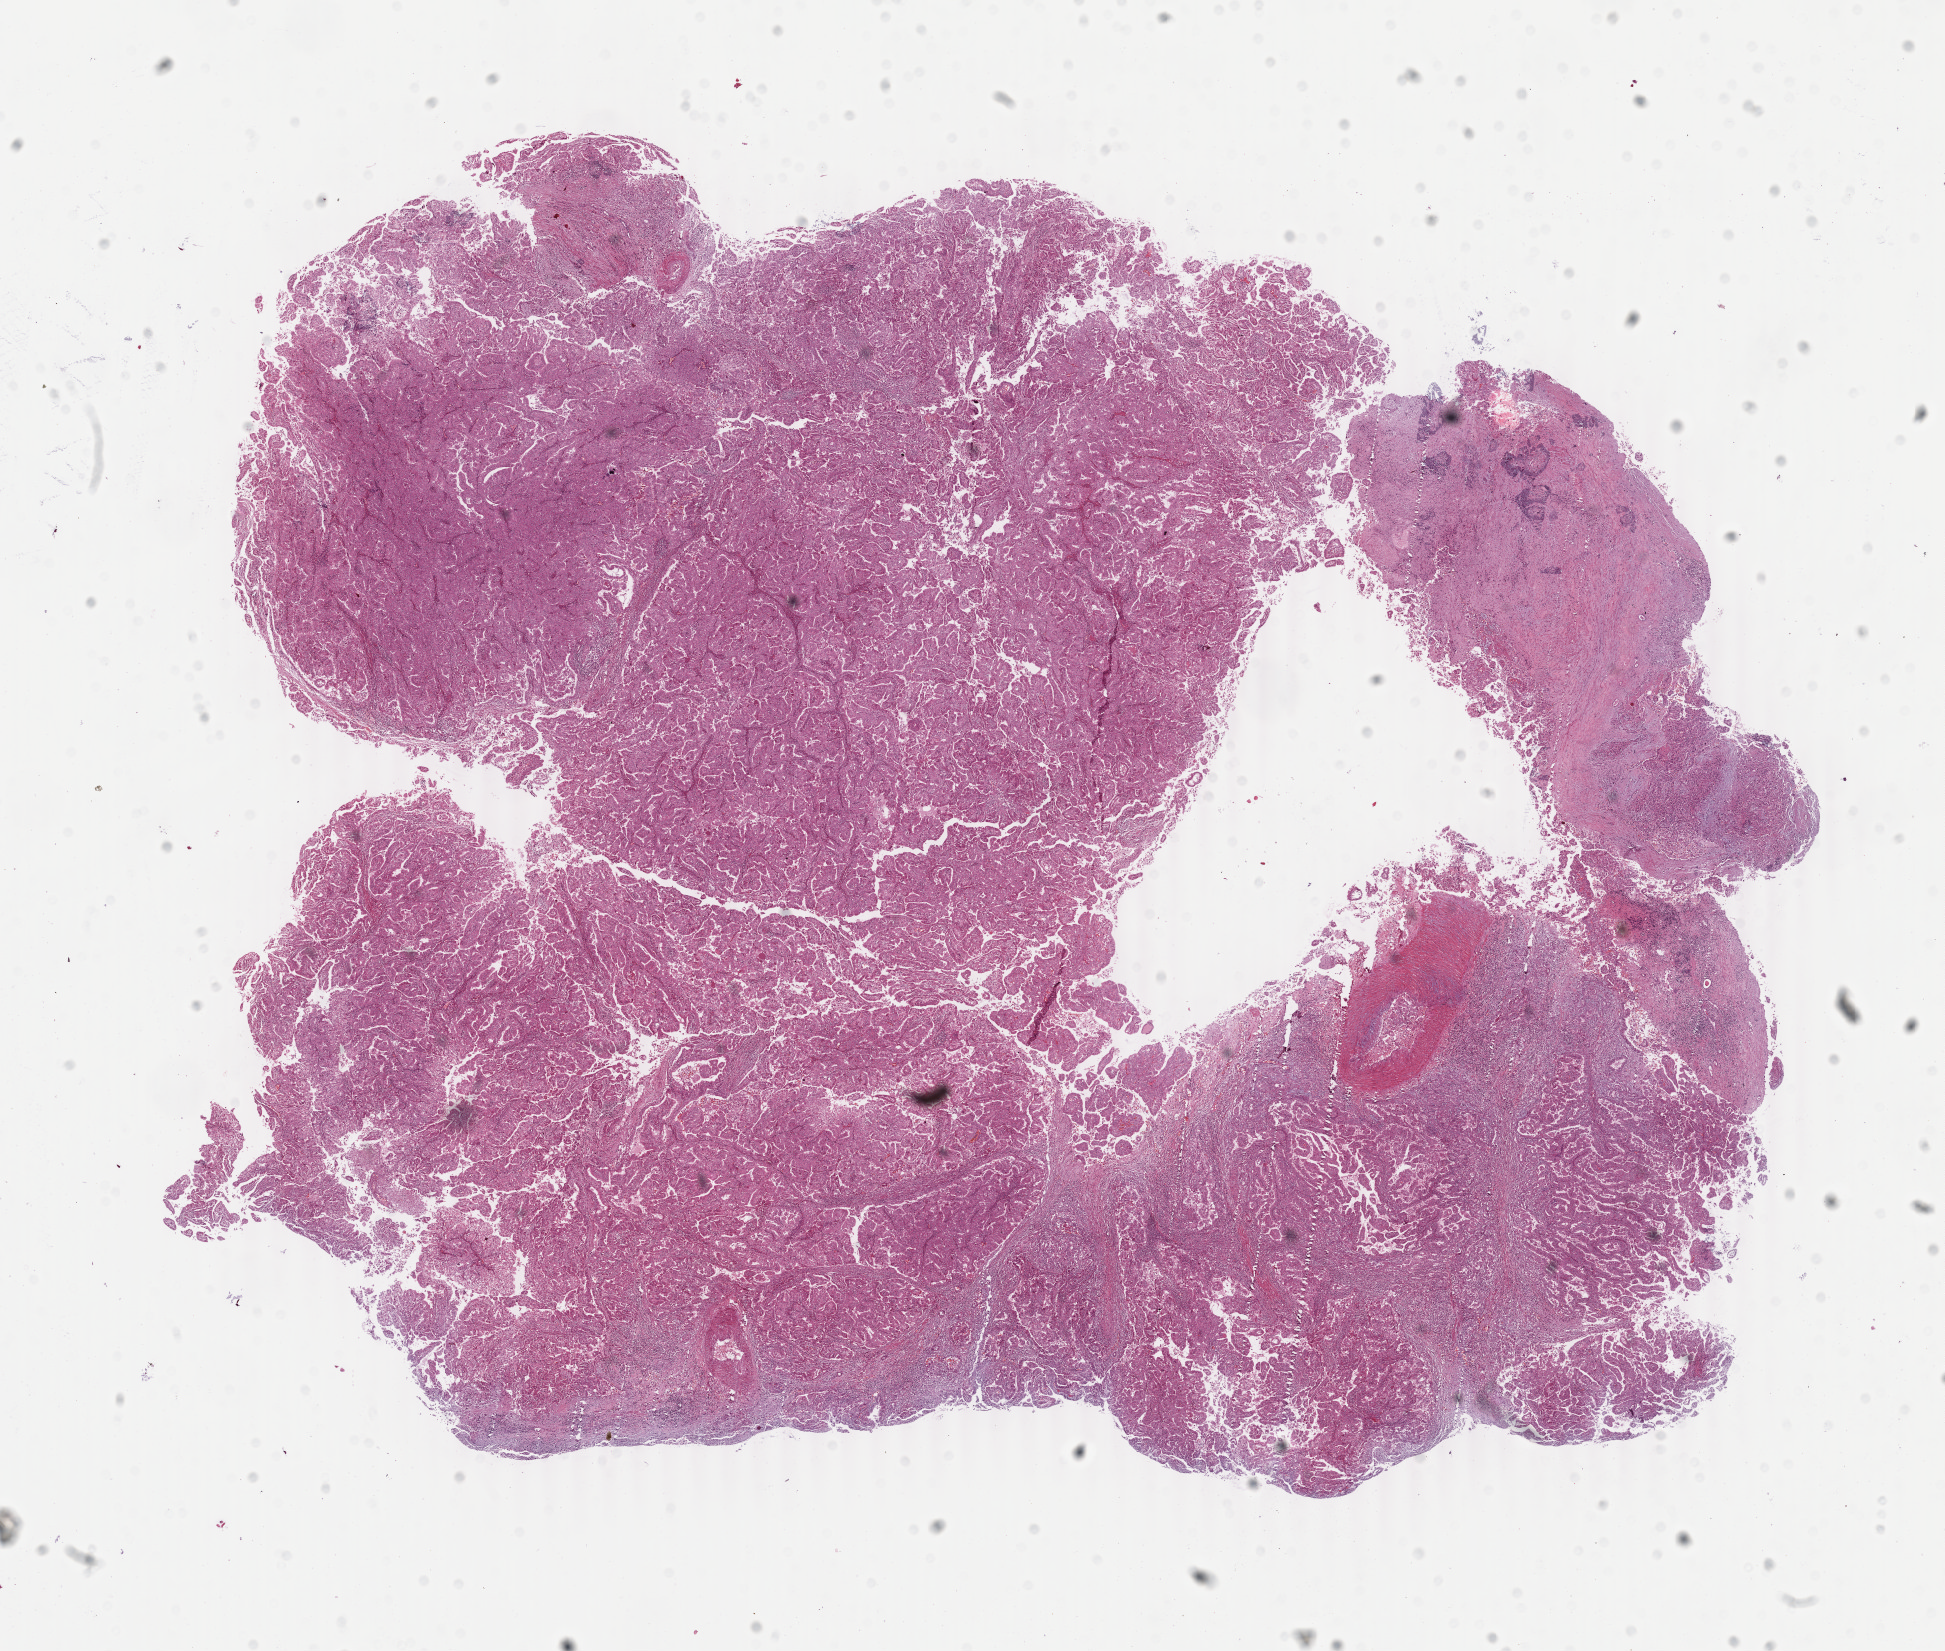
Hematoxylin and eosin (H&E) stained whole-slide image — whole scanned area (about 15.5 x 13.1 mm, slide scanned at 40x) shown as a low-resolution overview; formalin-fixed paraffin-embedded (FFPE) diagnostic section; primary tumour sample from the kidney. Female, age 37 years at initial diagnosis.
Histologic diagnosis: Papillary adenocarcinoma, NOS.